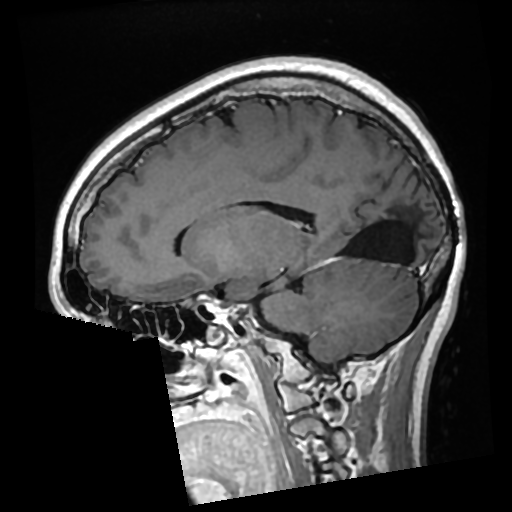
Brain MRI from a brain-tumour surgery series, one sagittal slice. Position 118 of 276 along the scan axis. T1-weighted post-contrast. 512 × 512 image matrix. From the clinical record (not read from this slice): histopathology: Glioma with ependymal features; WHO grade: 2; tumour location: Left Parietal.
Outlined on this slice (manually delineated by an expert):
- previous resection cavity: bounding box [x1, y1, x2, y2] px = [344, 200, 416, 262]